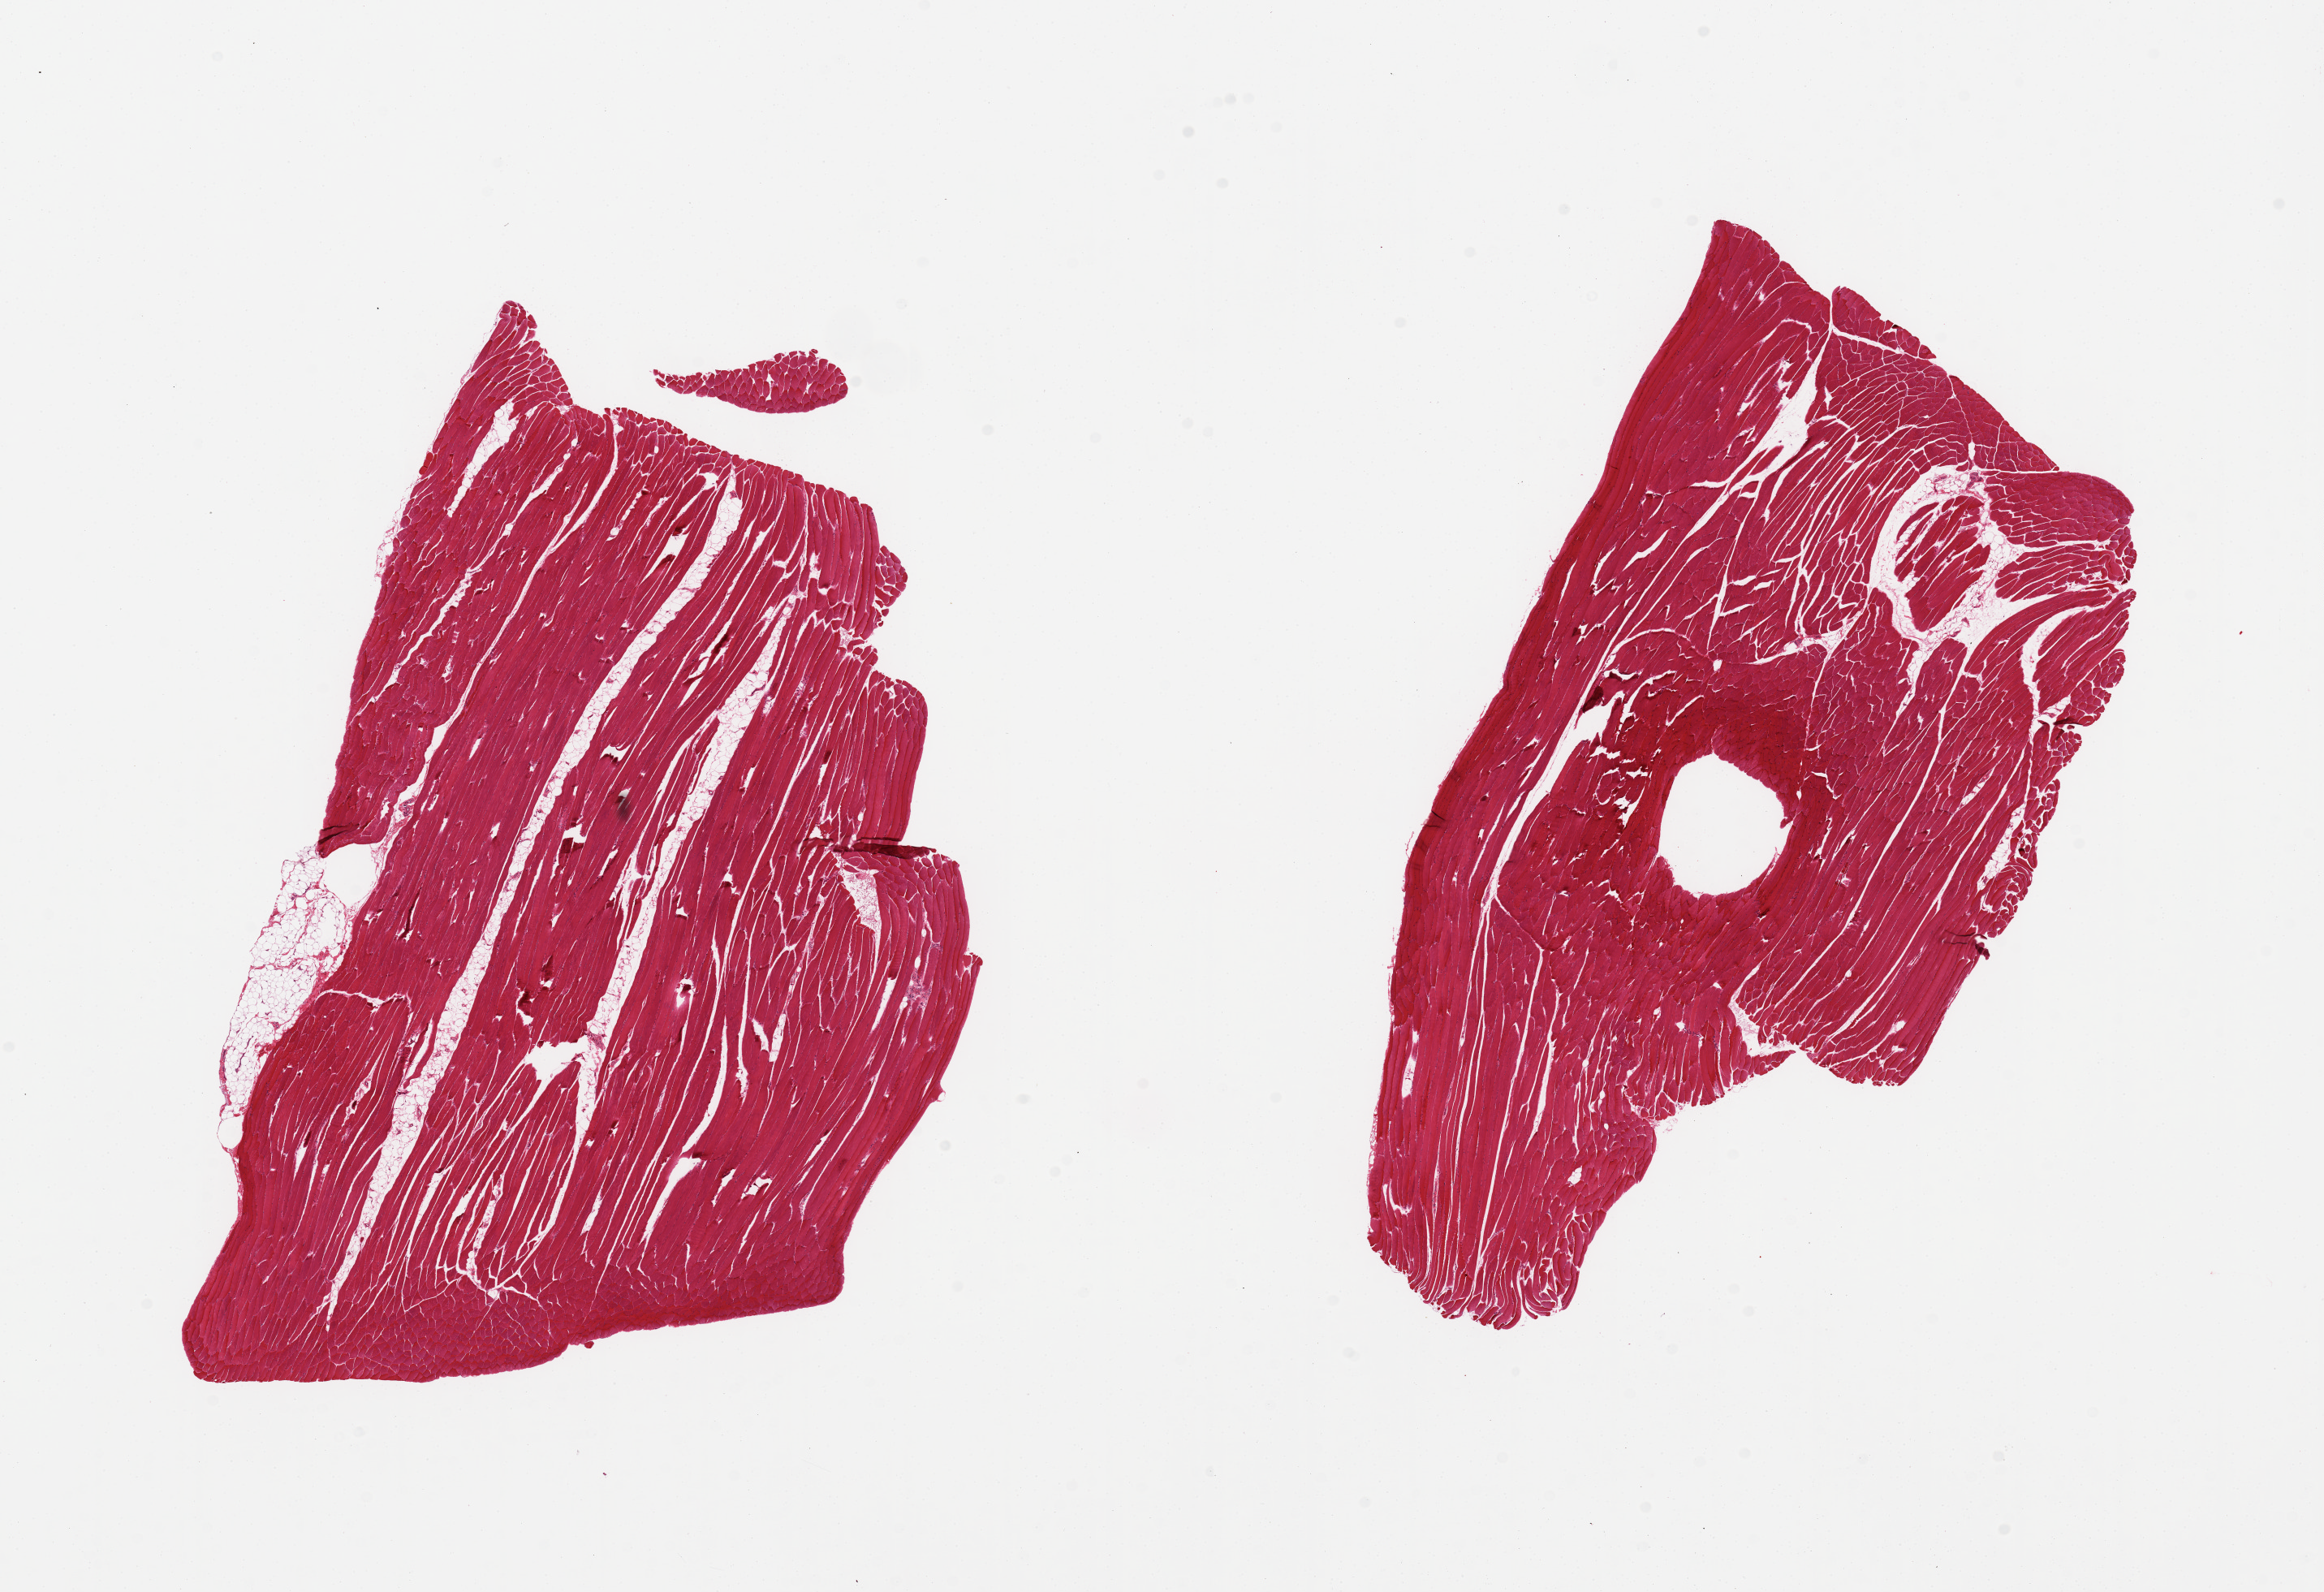
Digitized H&E-stained section, a low-resolution overview of the entire scanned area, about 22.6 x 15.5 mm; PAXgene-fixed paraffin-embedded (PFPE) section; section of skeletal muscle (target tissue); tissue donor sample. Male donor.
Reviewer comment on this tissue sample: 2 pieces, ~5-10% interstitial fat.